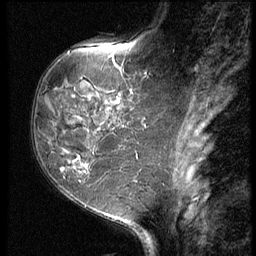
Breast MRI (dynamic contrast-enhanced), one sagittal slice. Slice 21 of 62 in the series (ordered by position). 3 images stored at this slice position (order not interpretable as contrast timing). 1.5 T. TE 4.2 ms, TR 9 ms. 256 × 256 image matrix. Female patient, age 50 years. Case-level facts recorded for this patient, not image findings: setting: breast cancer imaged before/during neoadjuvant chemotherapy; receptor status: HR-positive, HER2-negative.
Outlined on this slice (semi-automatic segmentation, software-assisted and operator-edited):
- analysis volume of interest (the breast-tissue region the enhancement analysis was run in; not a lesion): bounding box (x1, y1, x2, y2) in pixels: (32, 91, 118, 209)
- tumour enhancement mask (voxels above the 140 % enhancement threshold inside the analysis volume of interest): (62, 158, 81, 171)